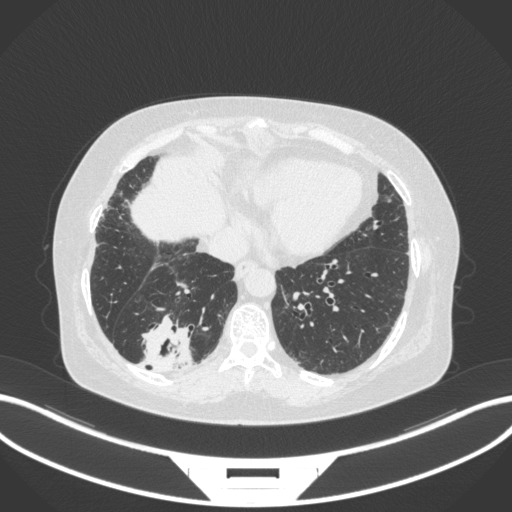
Chest CT, one axial slice. Slice 59 of 303 in the series (ordered by position). Reconstruction kernel B31f. Lung window (W 1500 / L -600 HU). 1 mm slice thickness. 512 × 512 image matrix, field of view 400 × 400 mm. Patient: female, 65 years. Case-level facts recorded for this patient, not image findings: clinical TNM (as recorded): T2b N1 M0.
Outlined on this slice (rectangle marked by the reading radiologist):
- lung tumour (recorded histology: adenocarcinoma): bounding box [x1, y1, x2, y2] px = [136, 314, 196, 375]